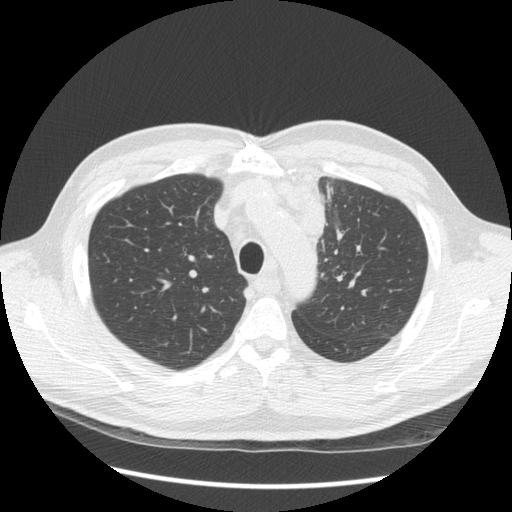
Low-dose screening chest CT, one axial slice. Slice 107 of 136 in the series (ordered by position). Reconstruction kernel STANDARD. 120 kVp. Lung window (W 1500 / L -600 HU). 2.5 mm slice thickness. 512 × 512 image matrix.
Annotated regions visible in this slice (outlined manually by an expert reader):
- lesion 1 (tumor, upper lobe of left lung): bounding box [x1, y1, x2, y2] px = [276, 175, 326, 245]